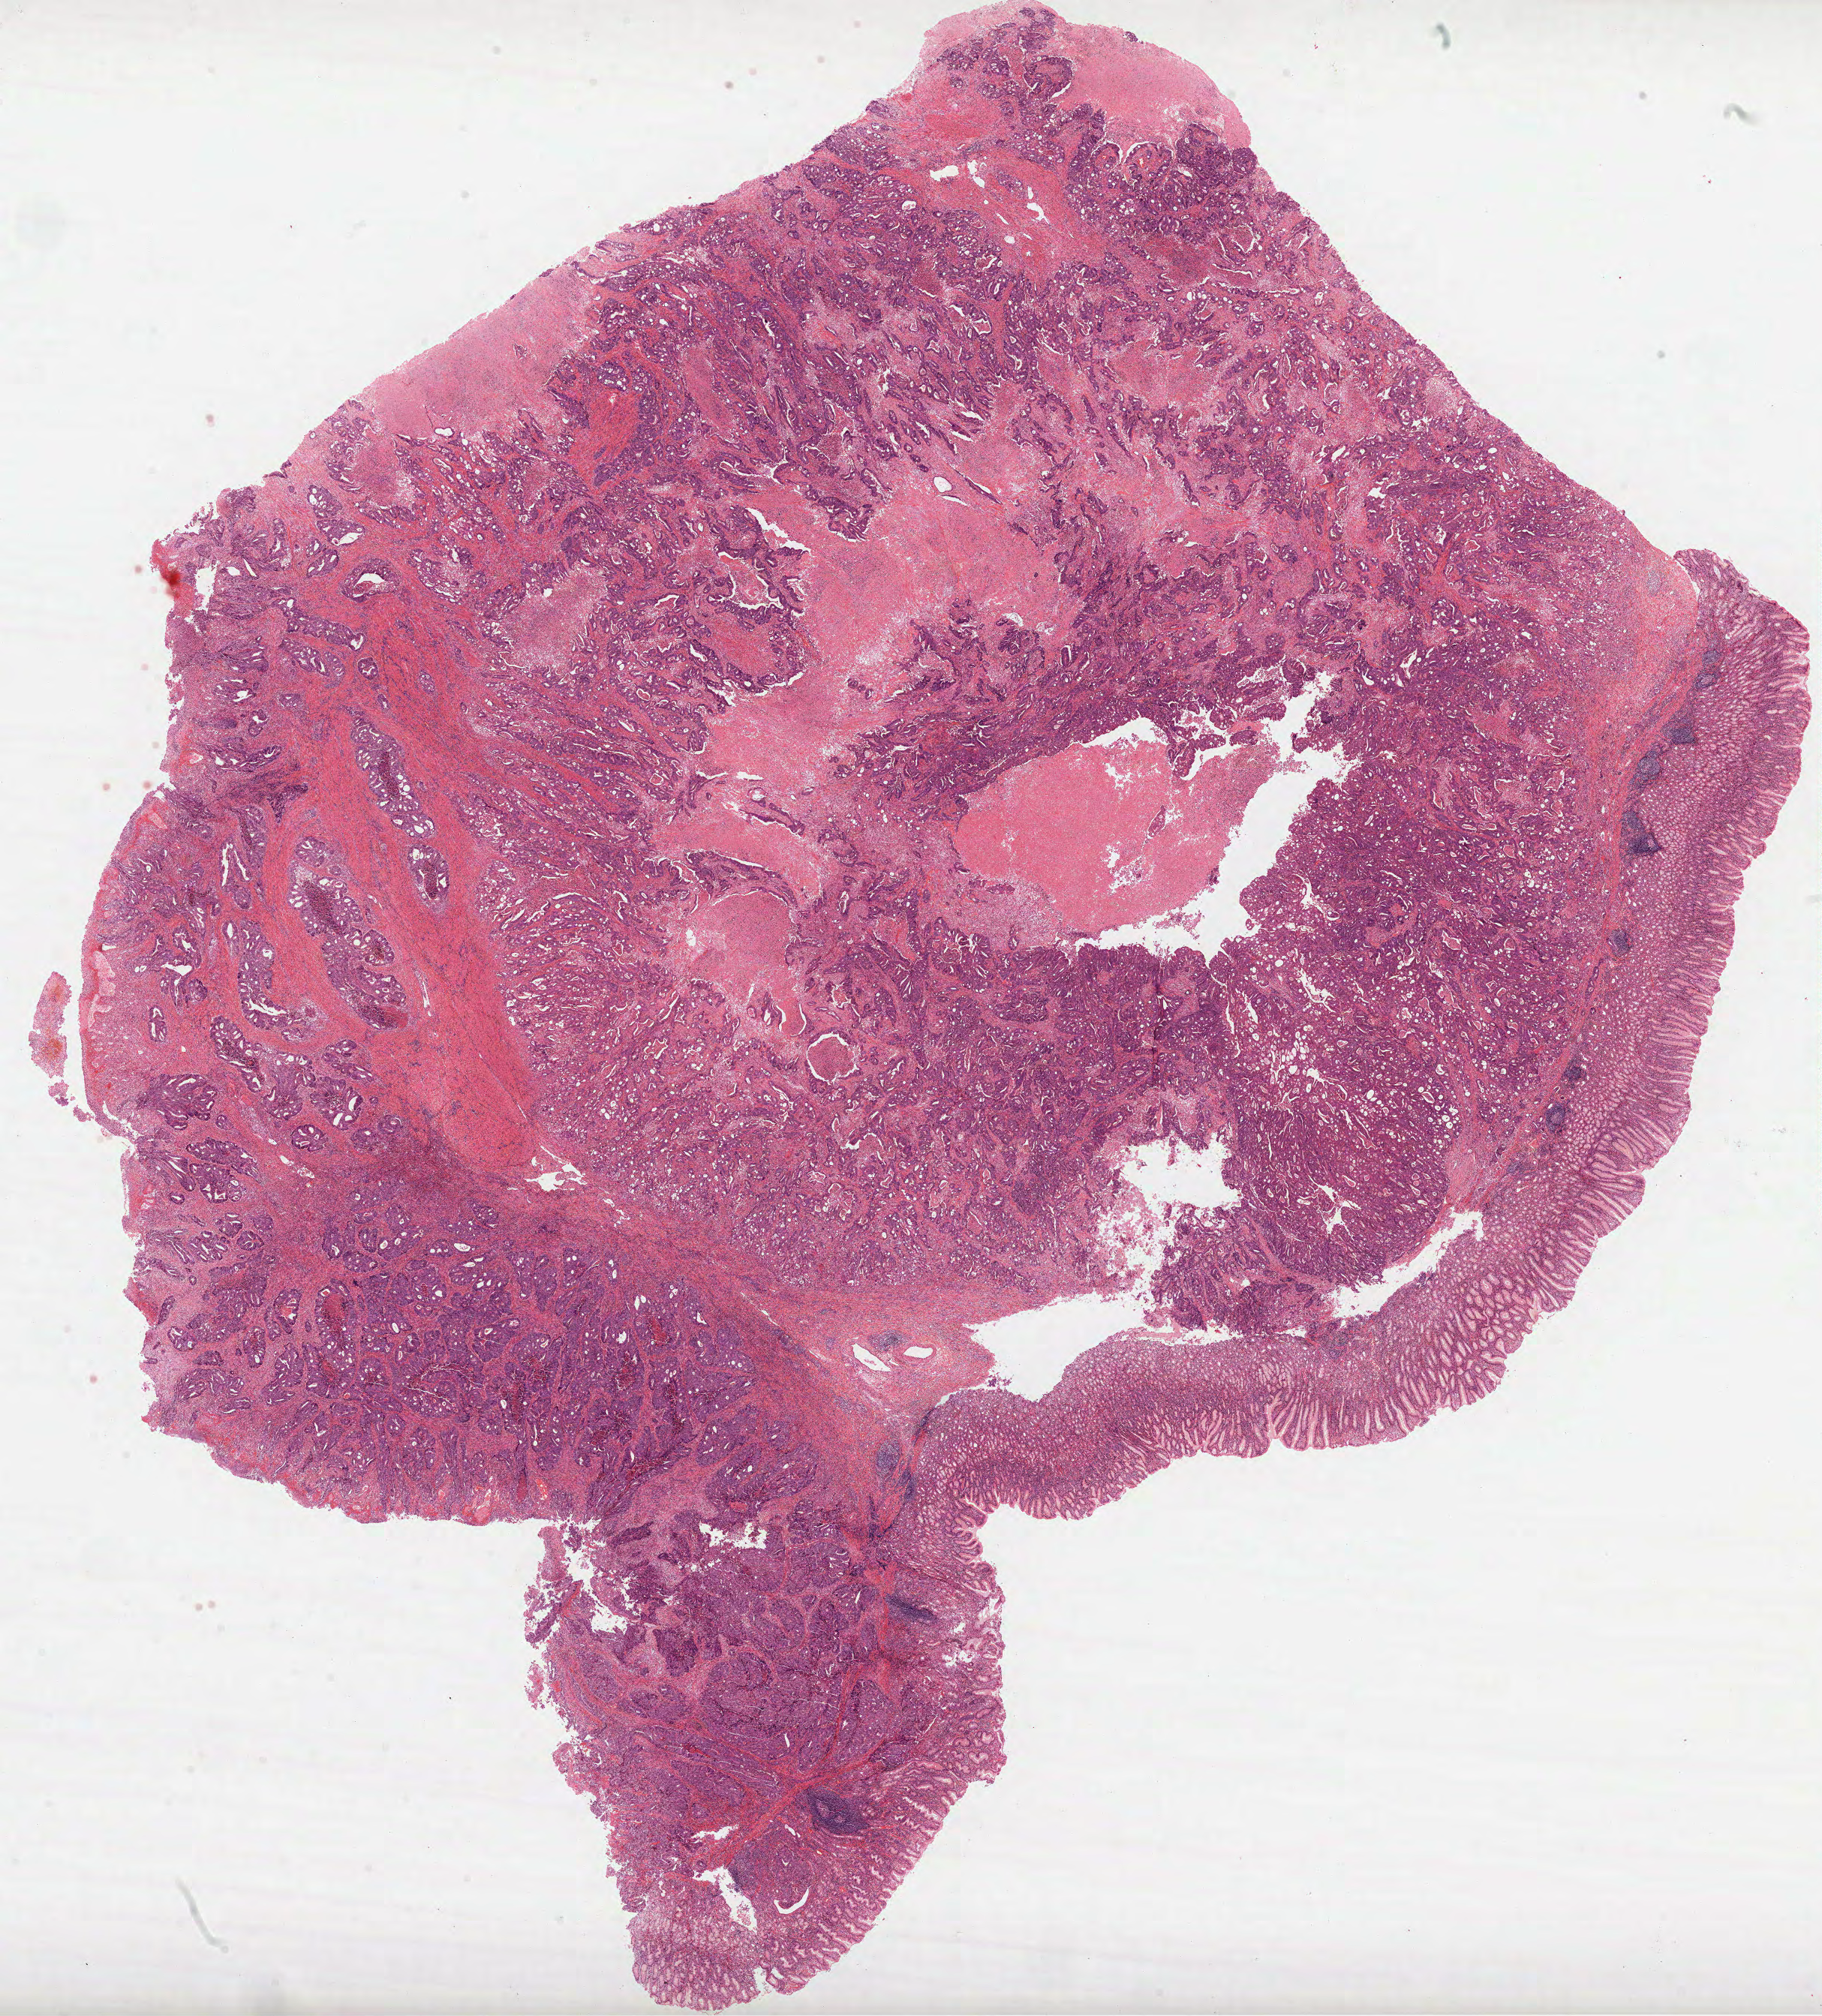
Whole-slide histology image, H&E-stained, whole scanned area (about 19.6 x 21.7 mm, slide scanned at 40x) shown as a low-resolution overview, FFPE section, stomach, primary tumour sample. Male, age 45 years at initial diagnosis. Histologic grade: G2 (moderately differentiated).
AJCC pathologic stage: IV (7th edition). Histologic diagnosis: Tubular adenocarcinoma (gastric antrum).